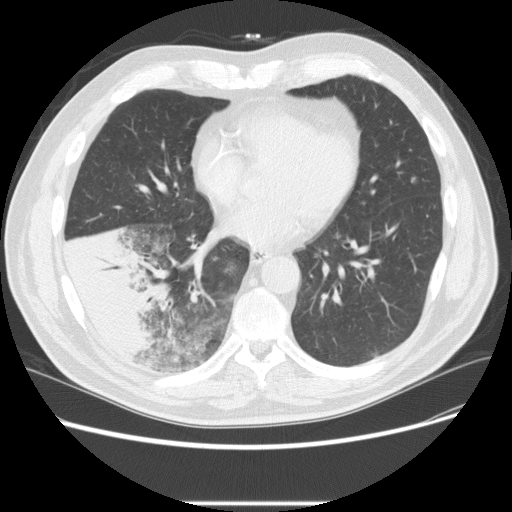
Low-dose screening chest CT, one axial slice; position 93 of 233 along the scan axis; reconstruction kernel STANDARD; lung window (W 1500 / L -600 HU); 512 × 512 image matrix, field of view 380 × 380 mm.
Annotated regions visible in this slice (expert manual segmentation):
- lesion 3 (tumor, lower lobe of right lung): box from (x=65, y=227) to (x=169, y=352) px